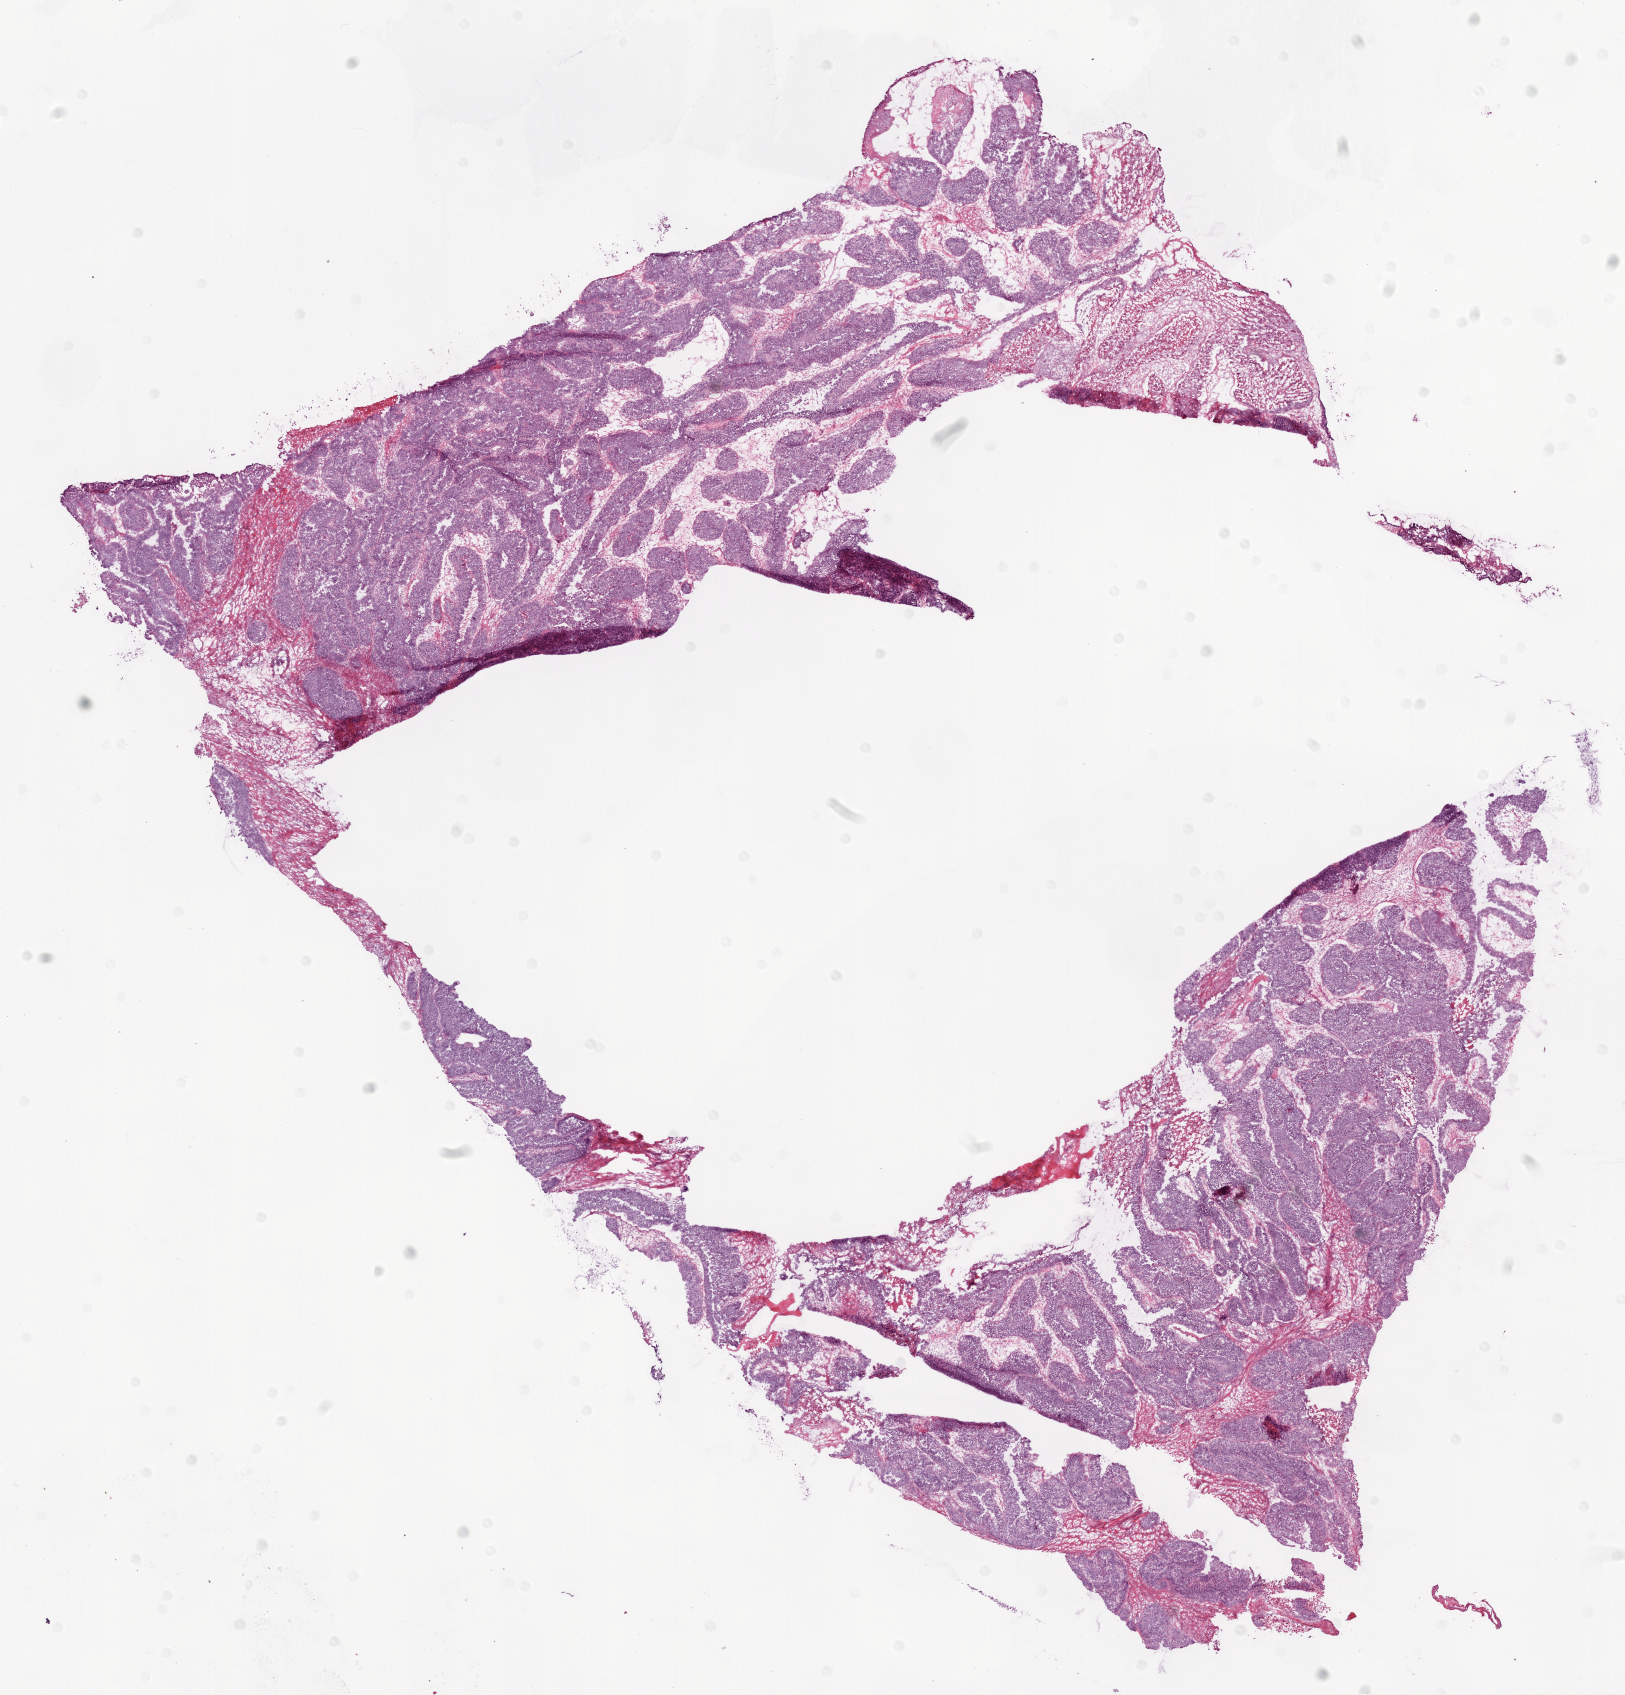
Hematoxylin and eosin (H&E) stained whole-slide image, a low-resolution overview of the entire scanned area, about 13.0 x 13.6 mm (slide scanned at 20x). Frozen section. Primary tumour sample from the ovary. Female, age 78 years at initial diagnosis. Histologic grade: G3 (poorly differentiated). Composition of this section per pathologist review: tumour cells 95%, tumour nuclei 90%, normal cells 0%, stromal cells 0%, necrosis 5%.
FIGO stage: IC. Laterality: left. Histologic diagnosis: Serous cystadenocarcinoma, NOS.